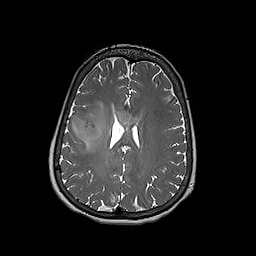
Brain MRI from a brain-tumour surgery series, one axial slice; position 78 of 192 along the scan axis; 1 mm slice thickness; 256 × 256 image matrix, field of view 250 × 250 mm. Case-level facts recorded for this patient, not image findings: histopathology: Oligodendroglioma; WHO grade: 3; IDH mutation: yes; tumour location: Right Frontal.
Structures marked on this image (expert manual segmentation):
- tumour: bounding box <72,115,104,143> (left, top, right, bottom; pixels)